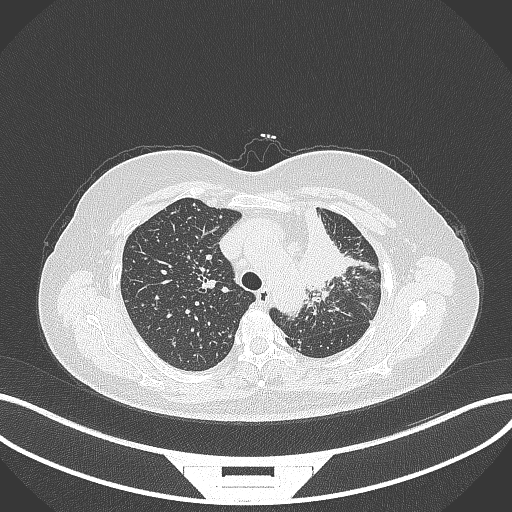
Chest CT, one axial slice. Position 249 of 348 along the scan axis. Reconstruction kernel B70f. 120 kVp. Lung window (W 1500 / L -600 HU). 1 mm slice thickness. 512 × 512 image matrix, field of view 400 × 400 mm. Female patient, age 49 years. From the clinical record (not read from this slice): clinical TNM (as recorded): T1c N0 M1.
Annotated regions visible in this slice (bounding box drawn by a radiologist):
- lung tumour (recorded histology: adenocarcinoma): box from (x=301, y=207) to (x=352, y=292) px